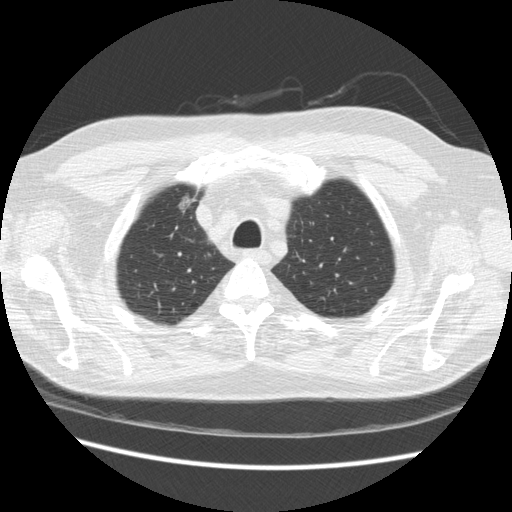
Low-dose screening chest CT, one axial slice; slice 192 of 234 in the series (ordered by position); reconstruction kernel STANDARD; 120 kVp; lung window (W 1500 / L -600 HU); 512 × 512 image matrix, field of view 360 × 360 mm.
Structures marked on this image (expert manual segmentation):
- lesion 1 (tumor, upper lobe of right lung): box from (x=179, y=193) to (x=196, y=214) px